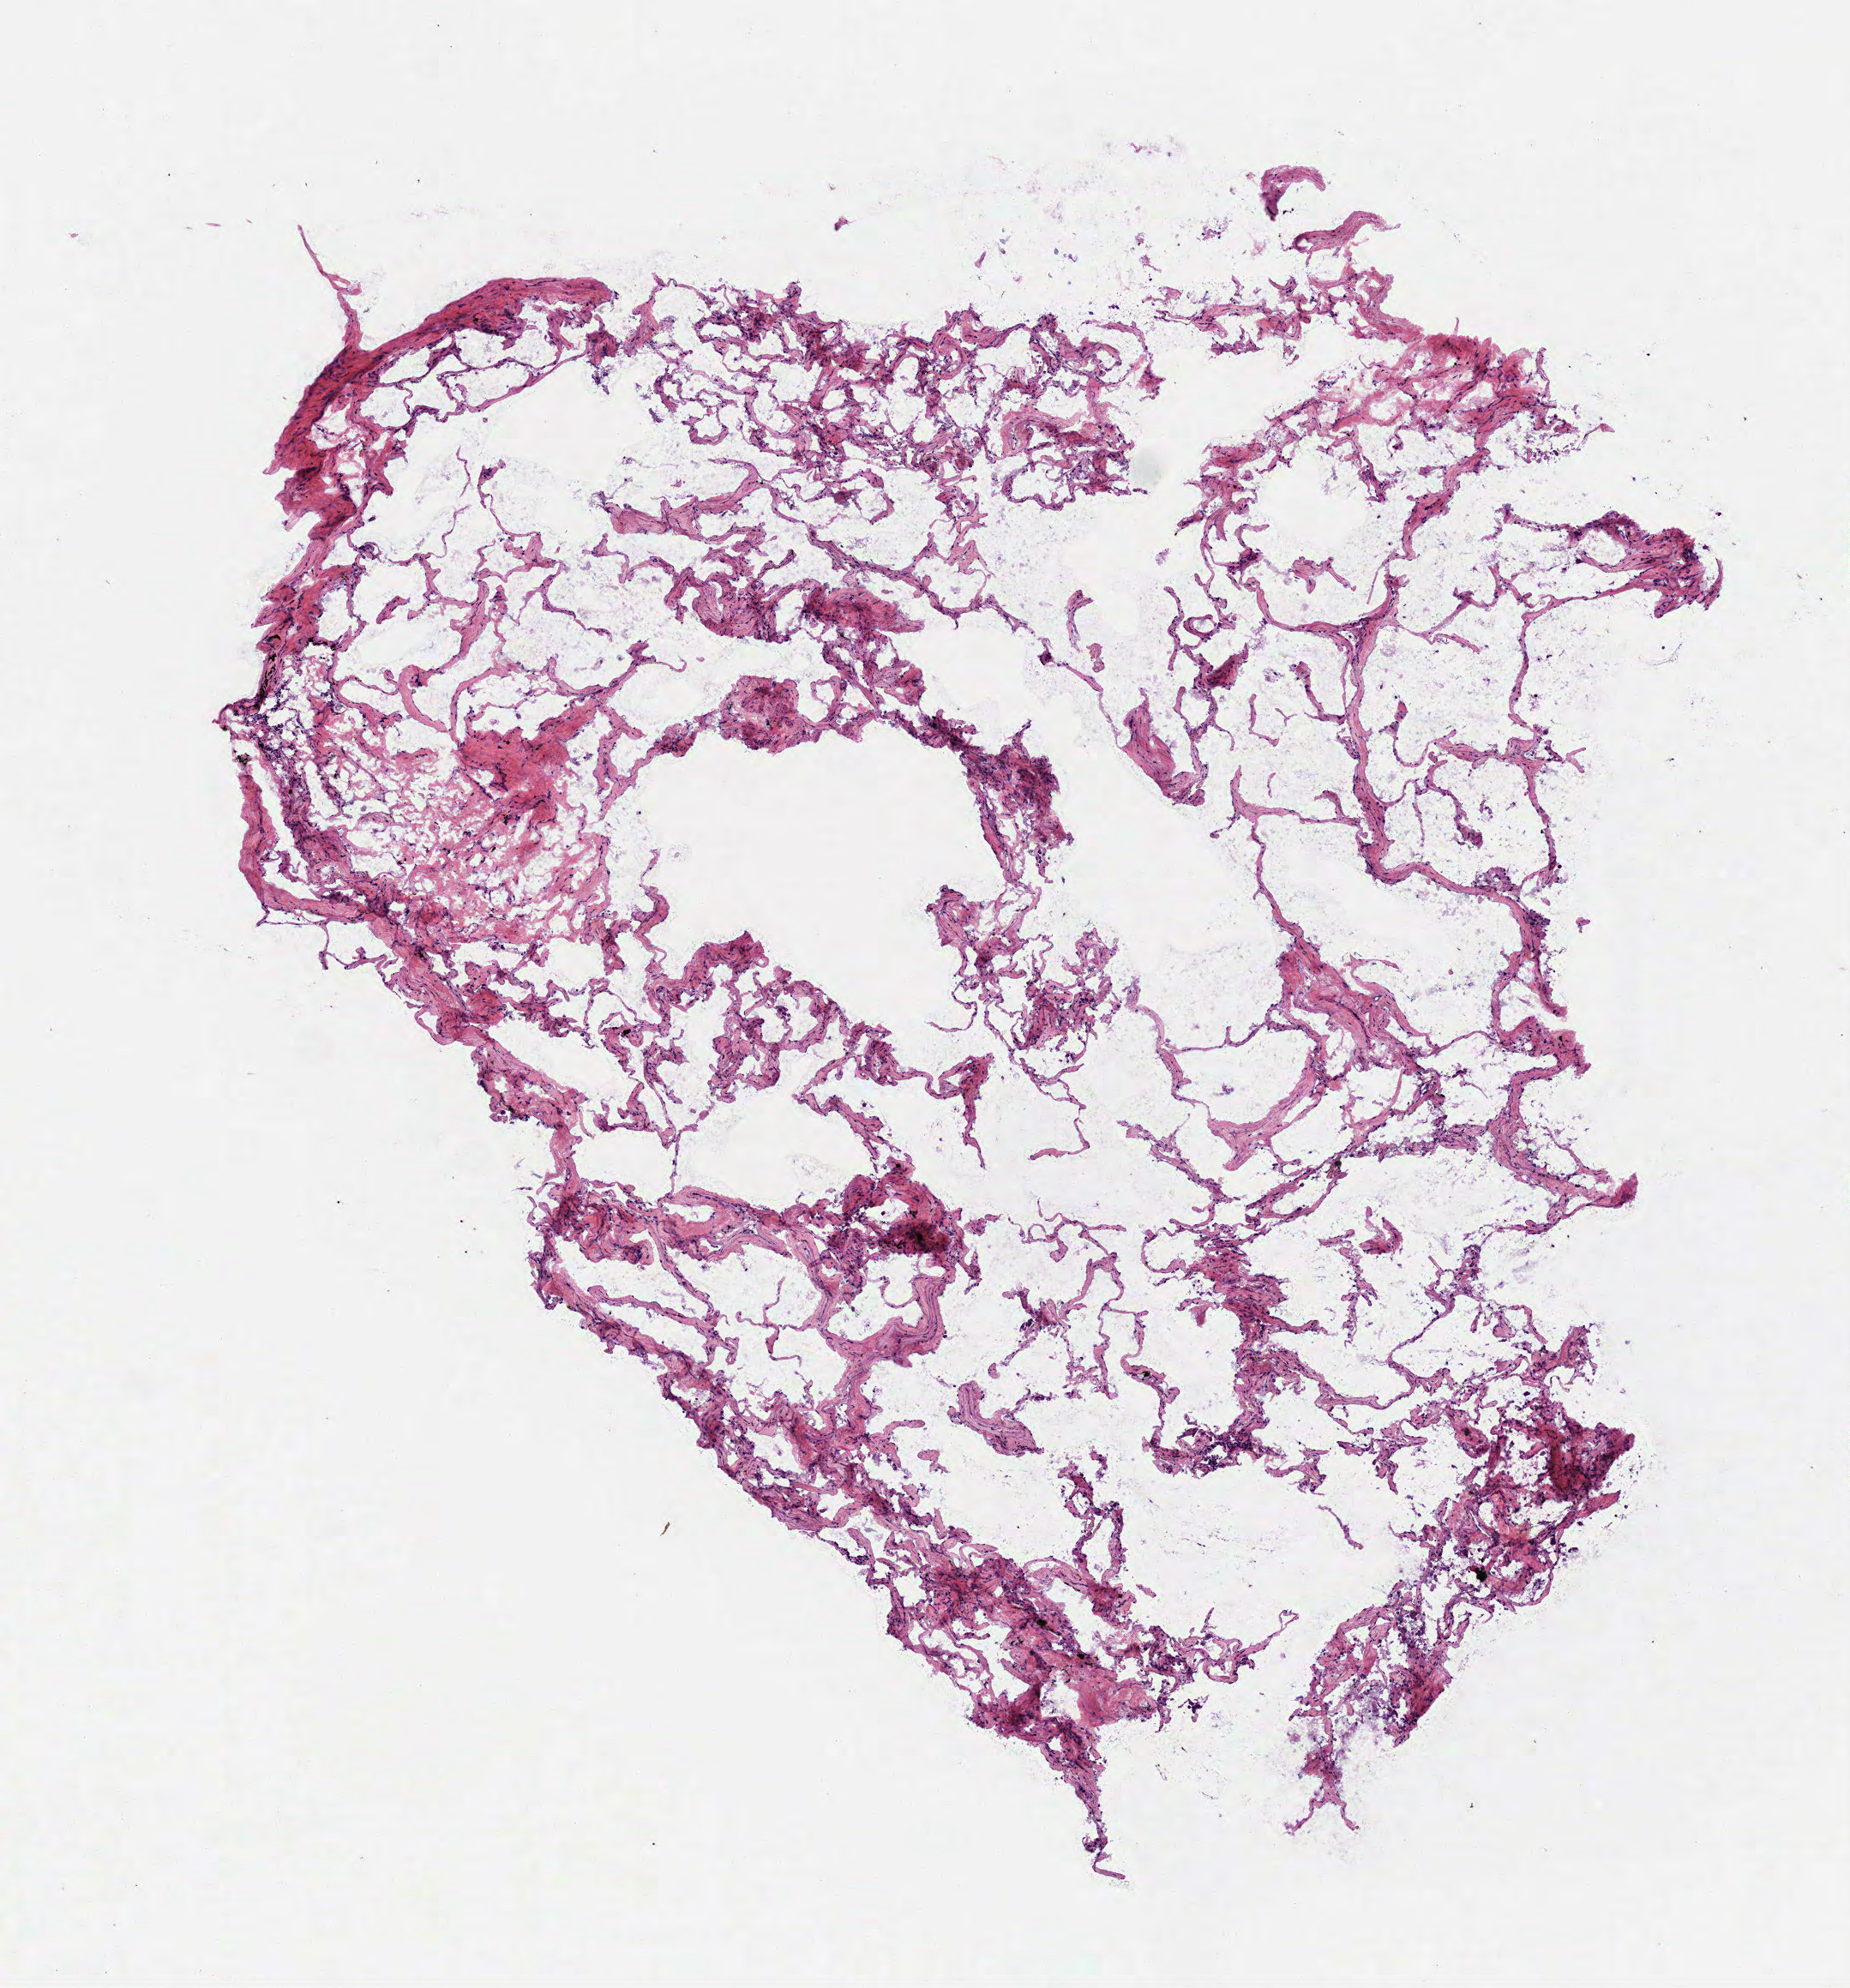
Whole-slide histology image, H&E, shown as a low-resolution overview of the whole scanned area (about 4.4 x 4.7 mm), frozen section from the top of the tissue portion, solid tissue normal (non-tumour tissue) sample from the lung. Patient: female, age at initial diagnosis 72 years. Infiltration values recorded for this section: lymphocyte infiltration 1%, monocyte infiltration 1%, neutrophil infiltration 0%.
This section: solid tissue normal sample (biorepository sample class). Patient diagnosis: Adenocarcinoma, NOS.